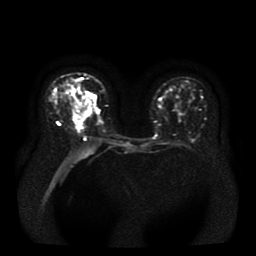
Breast MRI, one axial slice; slice 16 of 41 in the series (ordered by position); diffusion-weighted series; image 2 of 4 stored at this slice position (different b-values; order by instance number); 1.5 T; 5 mm slice thickness; 256 × 256 image matrix, field of view 330 × 330 mm. Female patient.
Structures marked on this image (outlined manually by an expert reader):
- tumour on diffusion-weighted imaging: bounding box <75,114,83,122> (left, top, right, bottom; pixels)